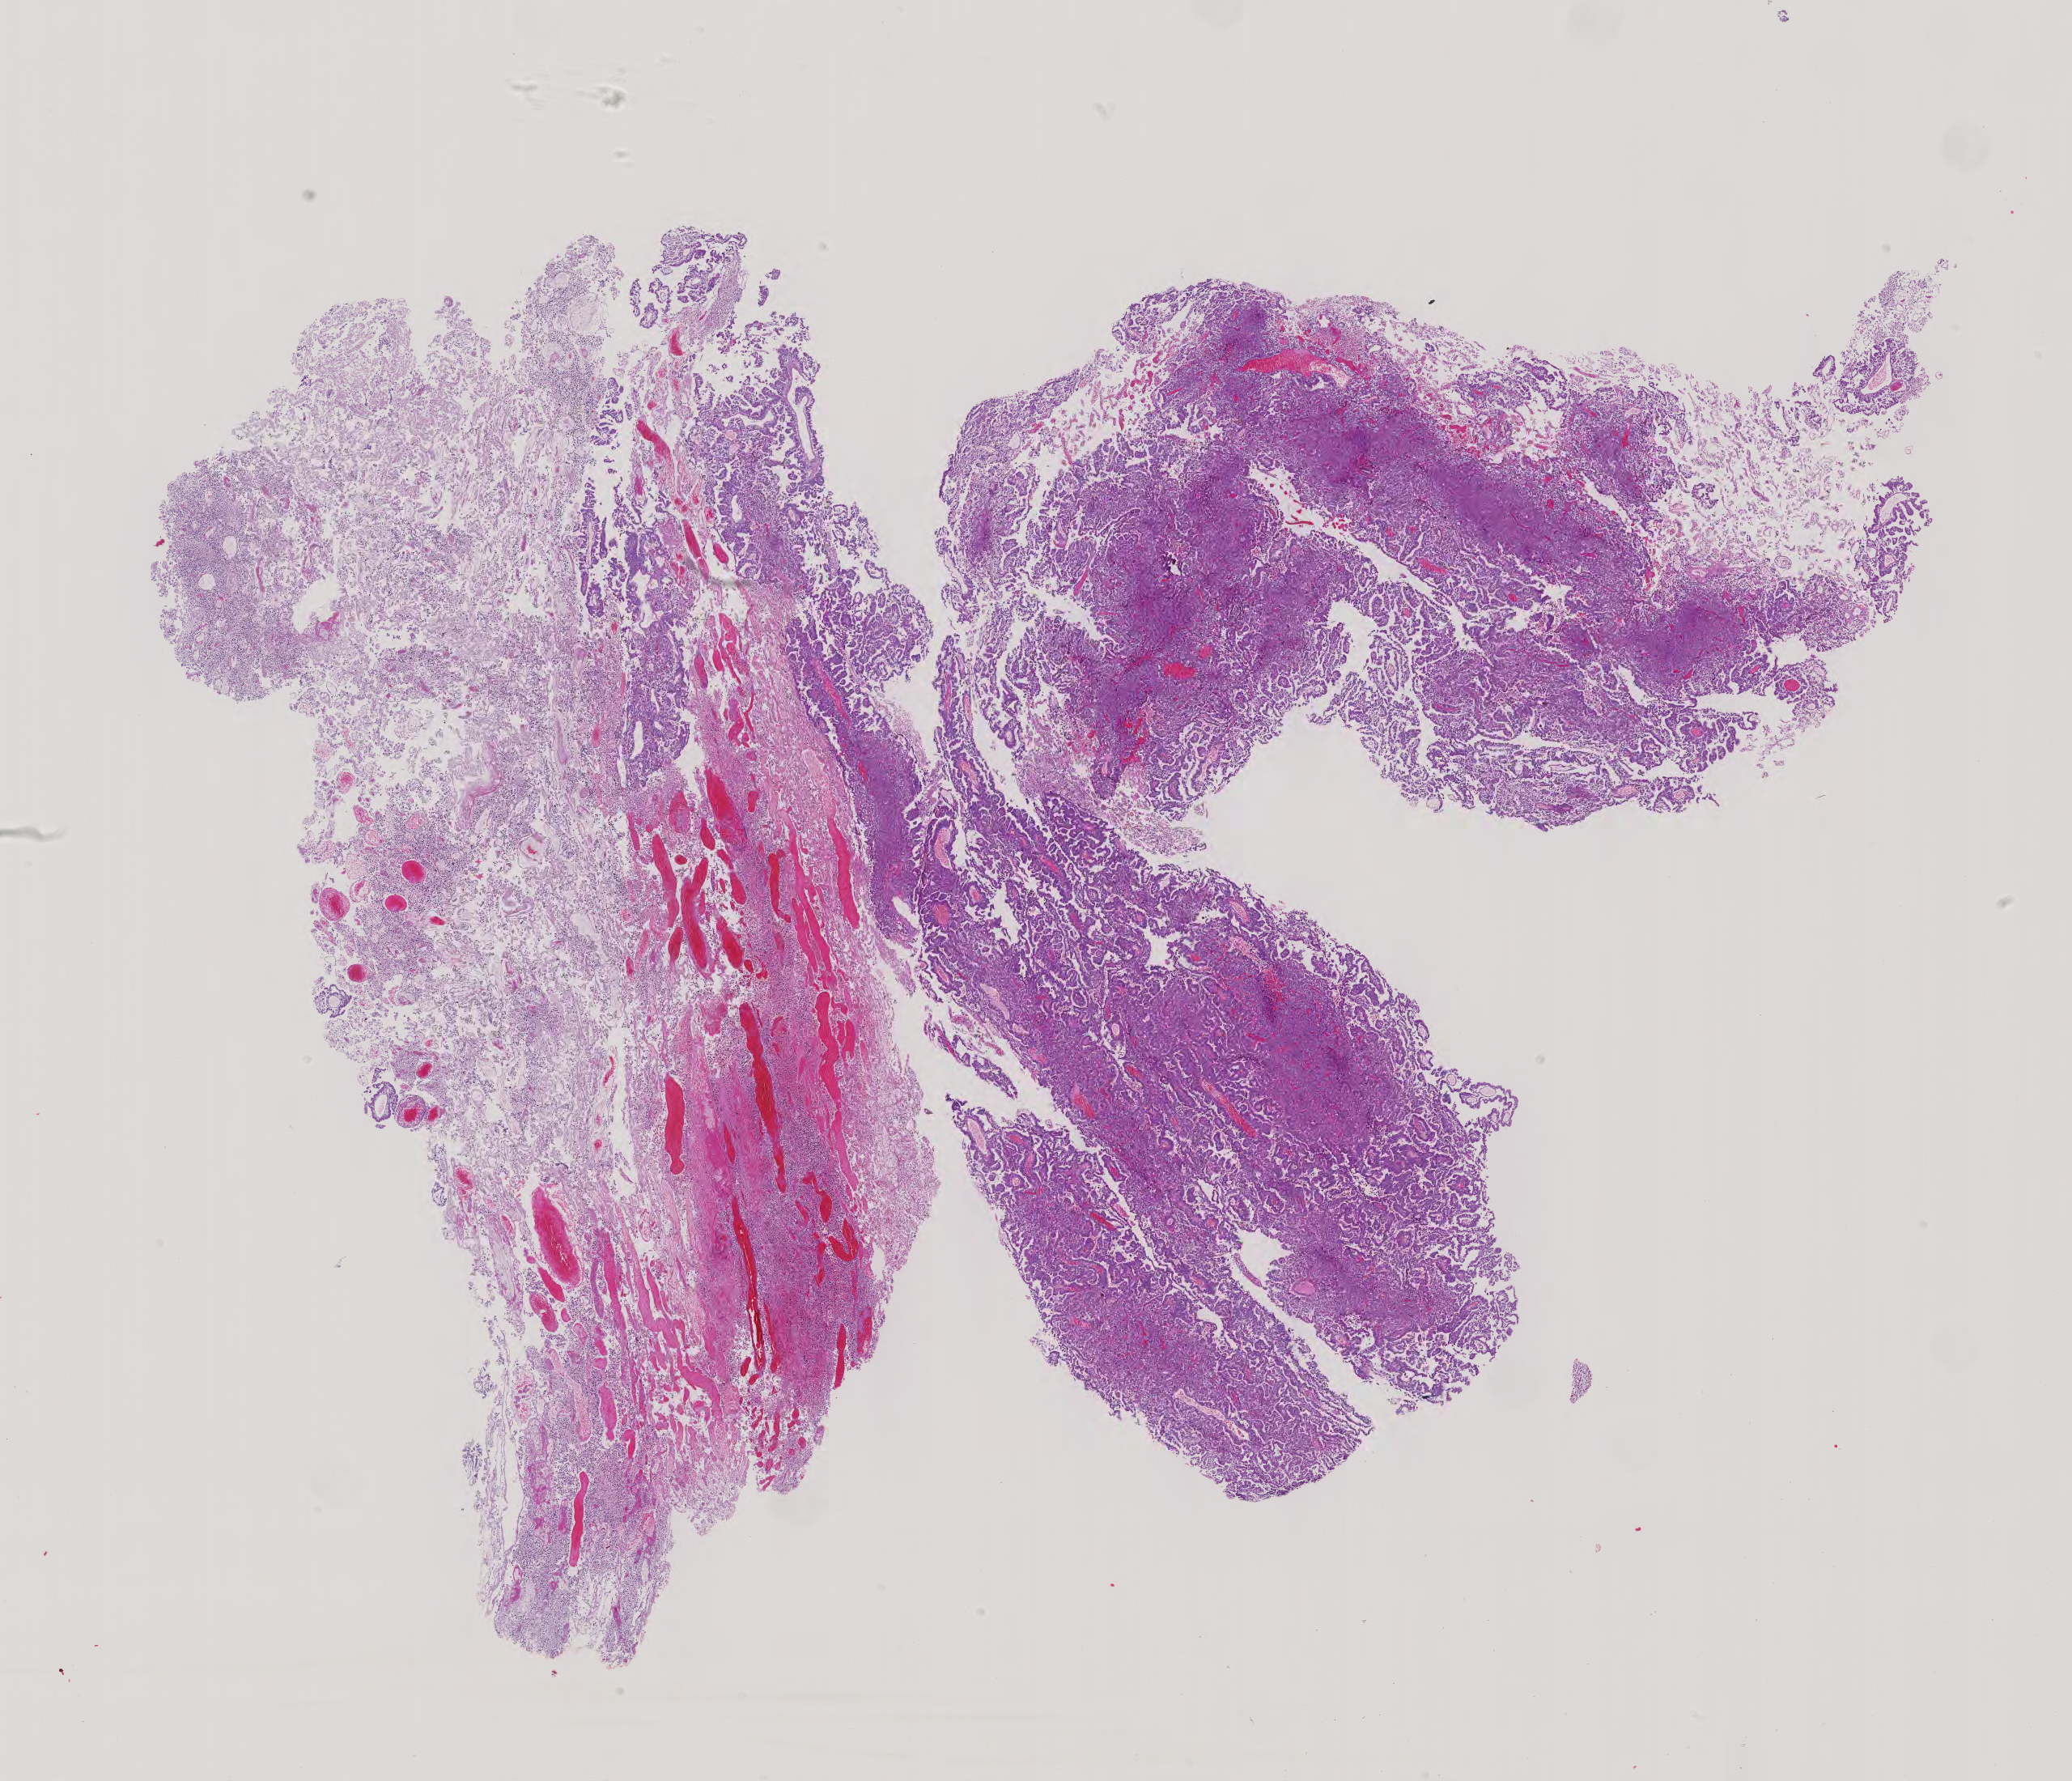
H&E whole-slide image, whole scanned area (about 18.7 x 16.0 mm, acquisition: 40x scan) shown as a low-resolution overview, formalin-fixed paraffin-embedded (FFPE) diagnostic section, primary tumour sample from the testis. Male patient; age at initial diagnosis 38 years.
AJCC pathologic stage: IS (5th edition). Diagnosis: Yolk sac tumor.